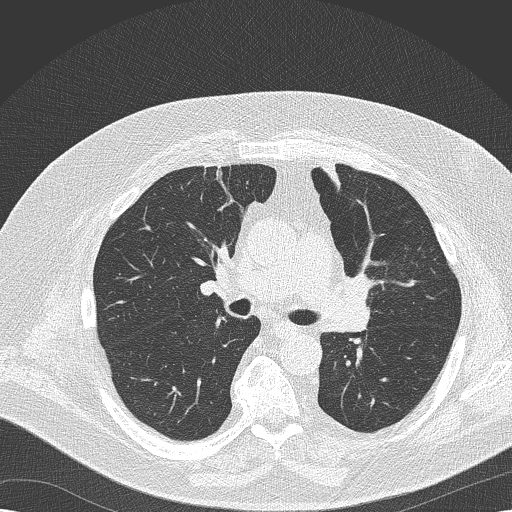
Low-dose screening chest CT, axial slice. Second screening round (one year after baseline). Lung window (W 1500 / L -600 HU). 2 mm slice thickness. Lung (sharp) reconstruction kernel (B50f). Slice 72 of 173 in the series. Male, age 68 years at enrolment. Former smoker at enrolment.
- Expert-annotated lung lesion, bounding box <321,263,385,324> (left, top, right, bottom; pixels).
- The exam's reader record, not a measurement of the box and not confirmed to be the same lesion: non-calcified nodule or mass ≥4 mm, left lower lobe, 8 × 6 mm, soft tissue attenuation, pre-existing on the prior screen: yes; interval growth: no.
- Official screen result: positive, no significant change: stable abnormalities potentially related to lung cancer, unchanged since the prior screening exam.
- Participant outcome: lung cancer diagnosed 256 days after this screen — squamous cell carcinoma, NOS, left upper lobe, poorly differentiated (G3), stage IIB (AJCC 6th edition), 35 mm at pathology.